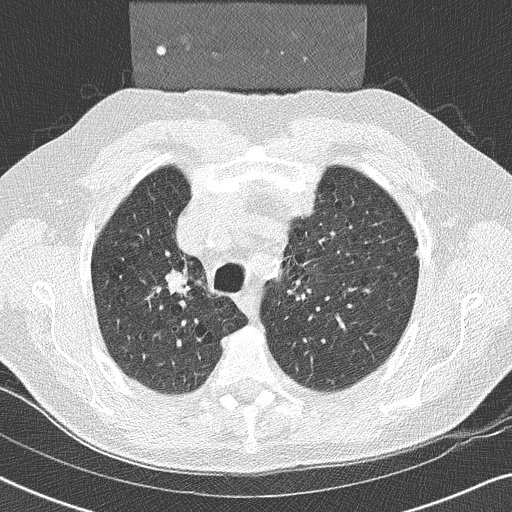
Low-dose screening chest CT, axial slice. Second annual screen. Lung window (W 1500 / L -600 HU). 2 mm slice thickness. 120 kVp. Slice 70 of 252 in the series. Male participant, aged 59 years at enrolment. Former smoker at enrolment.
Expert-annotated lung lesion, bounding box [x1, y1, x2, y2] px = [152, 259, 208, 307]. The exam's reader record, not a measurement of the box and not confirmed to be the same lesion: non-calcified nodule or mass ≥4 mm, right upper lobe, 17 × 16 mm, smooth margins, soft tissue attenuation, pre-existing on the prior screen: yes. Official screen result: positive, other. Lung cancer was diagnosed 14 days after this screen: squamous cell carcinoma, NOS, right upper lobe, poorly differentiated (G3), stage IIA (AJCC 6th edition), 20 mm at pathology.